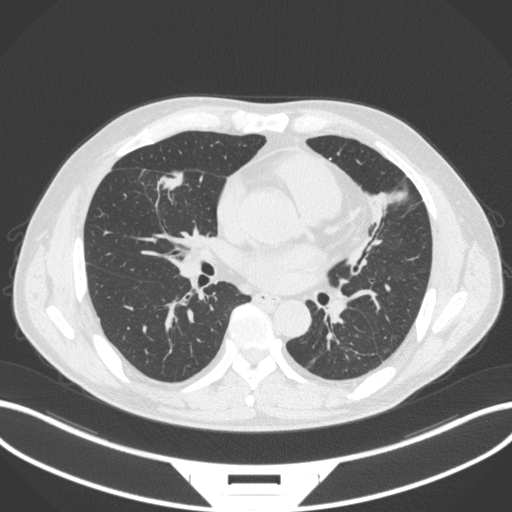
Chest CT, one axial slice; slice 150 of 399 in the series (ordered by position); 120 kVp; lung window (W 1500 / L -600 HU); 1 mm slice thickness; 512 × 512 image matrix, field of view 400 × 400 mm. Patient: male, 59 years. Case-level facts recorded for this patient, not image findings: clinical TNM (as recorded): T2a N1 M0.
Annotated regions visible in this slice (bounding box drawn by a radiologist):
- lung tumour (recorded histology: adenocarcinoma): bounding box [x1, y1, x2, y2] px = [158, 168, 187, 195]